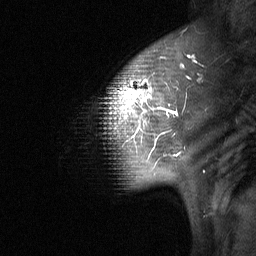
Breast MRI (dynamic contrast-enhanced), one sagittal slice. Slice 49 of 64 in the series (ordered by position). Dynamic contrast-enhanced study with each time point stored as its own series, time point 2 of 3 at this slice position (early post-contrast, ordered by acquisition time). 1.5 T. TE 4.8 ms, TR 27 ms. 256 × 256 image matrix, field of view 200 × 200 mm. Patient: female, 42 years. Case-level facts recorded for this patient, not image findings: setting: breast cancer imaged before/during neoadjuvant chemotherapy; receptor status: triple-negative.
Outlined on this slice (semi-automatically segmented with operator editing):
- analysis volume of interest (the breast-tissue region the enhancement analysis was run in; not a lesion): bounding box (x1, y1, x2, y2) in pixels: (104, 37, 203, 190)
- tumour enhancement mask (voxels above the 90 % enhancement threshold inside the analysis volume of interest): (110, 56, 196, 129)